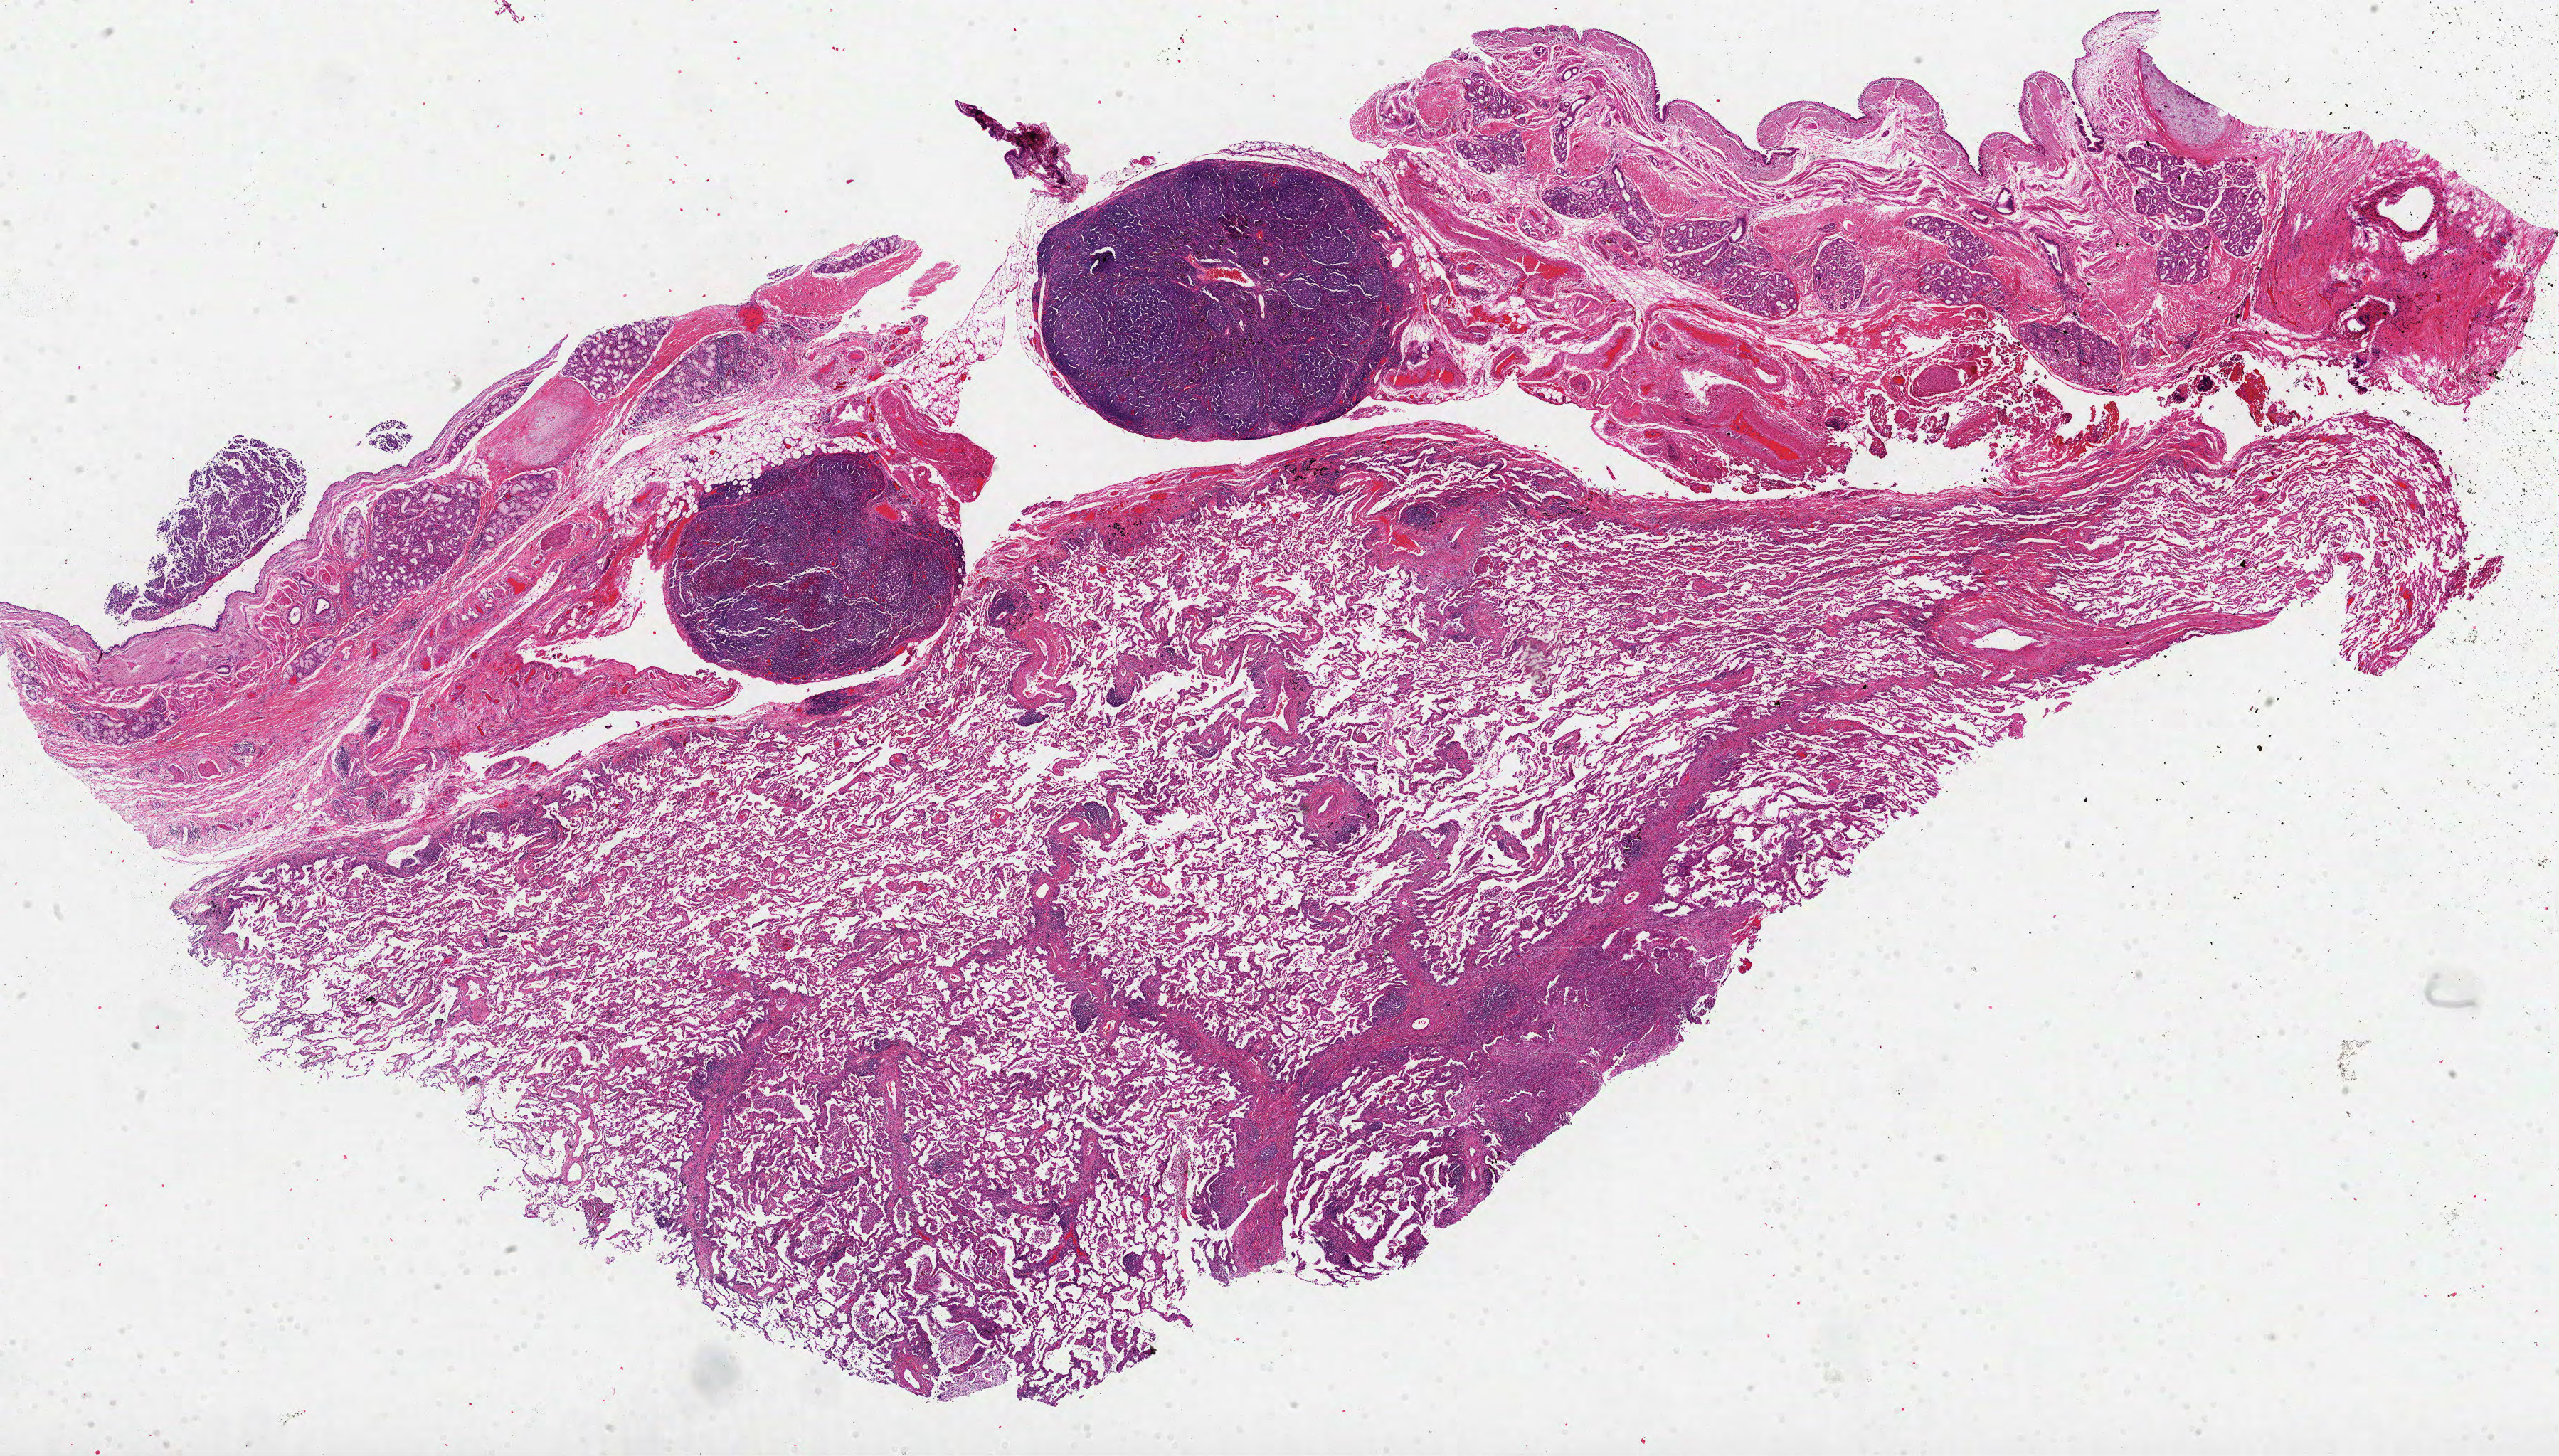
Digitized H&E tissue section (whole slide) — low-resolution overview of the scanned area, about 29.0 x 16.5 mm; formalin-fixed paraffin-embedded (FFPE) diagnostic section; primary tumour sample from the lung. Female patient; age at initial diagnosis 73 years.
Diagnosis: Adenocarcinoma, NOS (main bronchus). AJCC pathologic stage: IIIA. TNM: T3 N1 M0.